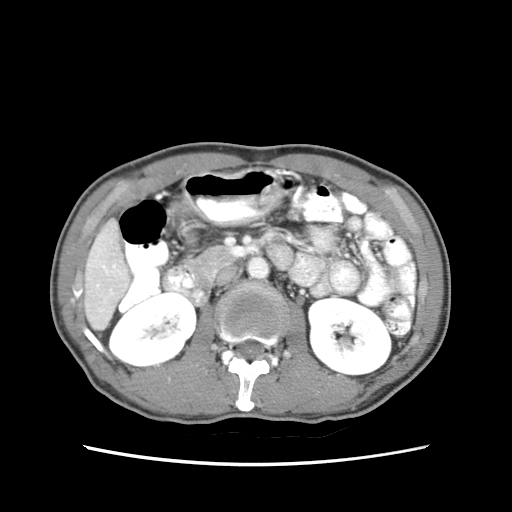
Contrast-enhanced abdominal CT (liver protocol), one axial slice. Position 18 of 79 along the scan axis. Reconstruction kernel STANDARD. 120 kVp. Soft-tissue window (W 400 / L 40 HU). 2.5 mm slice thickness. 512 × 512 image matrix, field of view 320 × 320 mm. From the clinical record (not read from this slice): diagnosis: hepatocellular carcinoma (patient treated with transarterial chemoembolisation; whether this scan precedes or follows treatment is not stated here); TNM stage (as recorded): Stage-IIIB; Child-Pugh class: A; tumour differentiation: moderately differentiated; tumour nodularity: multinodular.
Outlined on this slice (semi-automatic segmentation, software-assisted and operator-edited):
- liver parenchyma outside the tumour (the mass and vessels are separate outlines, so this box may not span the whole liver): bounding box <84,220,130,328> (left, top, right, bottom; pixels)
- liver vessels: <96,239,125,311>